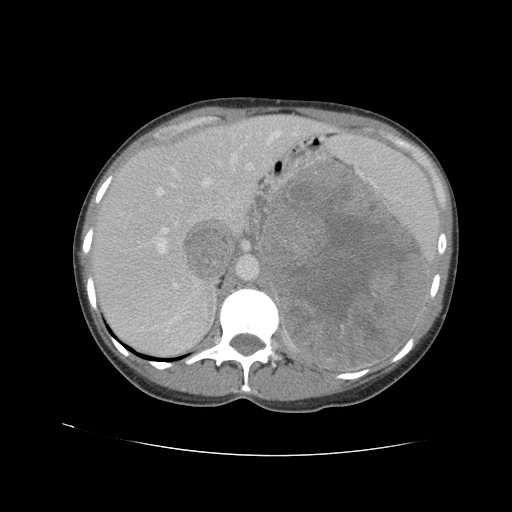
Contrast-enhanced abdominal CT, one axial slice; slice 70 of 90 in the series (ordered by position); reconstruction kernel STANDARD; intravenous contrast given; soft-tissue window (W 400 / L 40 HU); 5 mm slice thickness; 512 × 512 image matrix, field of view 360 × 360 mm. Female patient. Case-level facts recorded for this patient, not image findings: diagnosis: adrenocortical carcinoma; tumour side: left adrenal; tumour size at pathology: 18 cm; Ki-67 index: 11 %; stage (as recorded): 3.
Annotated regions visible in this slice (semi-automatic segmentation, software-assisted and operator-edited):
- mass: bounding box [x1, y1, x2, y2] px = [262, 163, 429, 369]